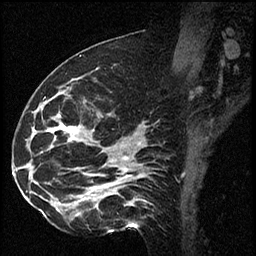
Breast MRI (dynamic contrast-enhanced), one sagittal slice; slice 32 of 60 in the series (ordered by position); dynamic contrast-enhanced series, image 2 of 2 at this slice position (ordered by acquisition); 1.5 T; TE 4.2 ms, TR 17.3 ms; 2 mm slice thickness; 256 × 256 image matrix, field of view 200 × 200 mm. Female patient. Case-level facts recorded for this patient, not image findings: setting: breast cancer imaged before/during neoadjuvant chemotherapy; receptor status: HR-positive, HER2-negative.
Outlined on this slice (semi-automatic segmentation, software-assisted and operator-edited):
- analysis volume of interest (the breast-tissue region the enhancement analysis was run in; not a lesion): bounding box [x1, y1, x2, y2] px = [41, 93, 115, 223]
- tumour enhancement mask (voxels above the 100 % enhancement threshold inside the analysis volume of interest): [56, 127, 77, 139]